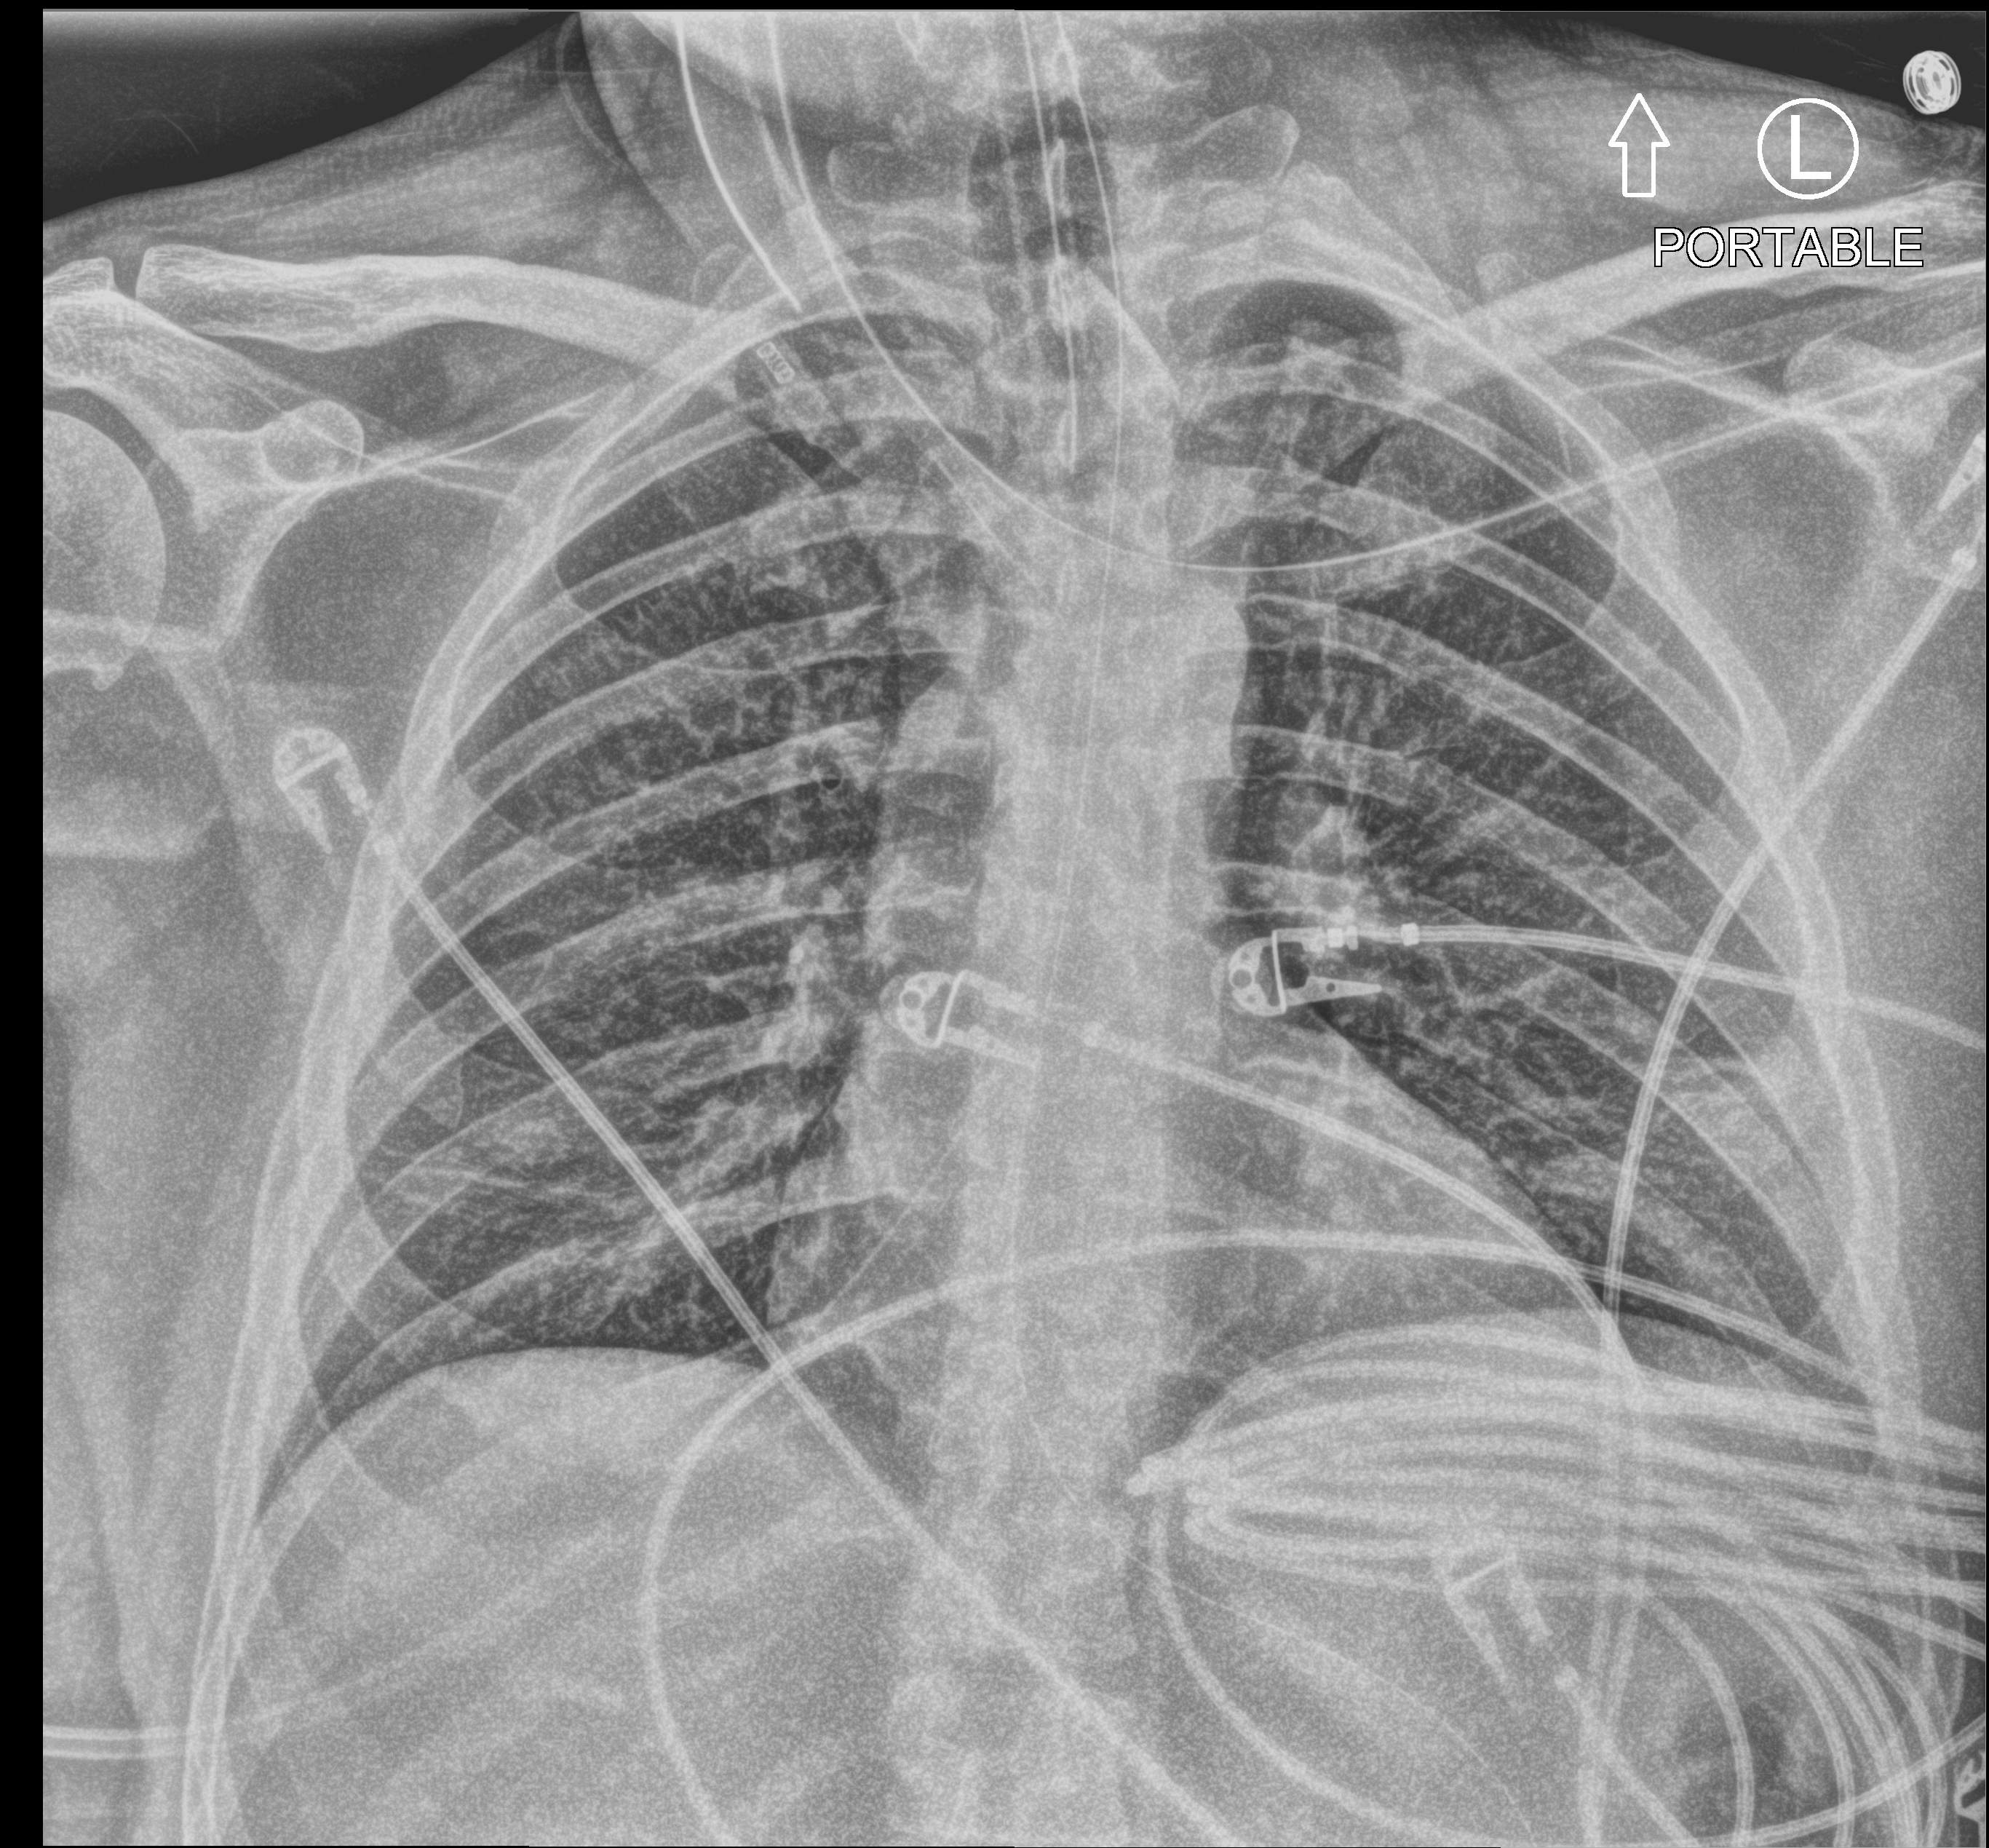
Portable chest radiograph. Male patient hospitalised with COVID-19, age 18–59 years.
From the hospital-stay record, not from the radiograph (when in the stay this image was taken is not recorded): hypertension (admission record): no; admitted to intensive care during this hospital stay: yes; mechanically ventilated during this hospital stay: yes.